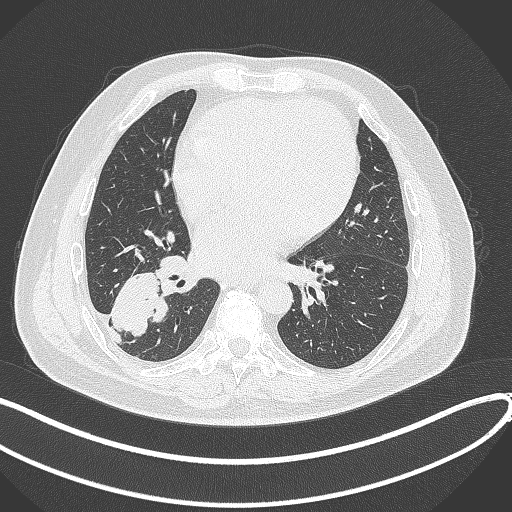
Chest CT, one axial slice; slice 155 of 360 in the series (ordered by position); reconstruction kernel B70f; lung window (W 1500 / L -600 HU); 1 mm slice thickness; 512 × 512 image matrix. Patient: male, 59 years.
Structures marked on this image (rectangle marked by the reading radiologist):
- lung tumour (recorded histology: adenocarcinoma): box from (x=107, y=266) to (x=167, y=341) px